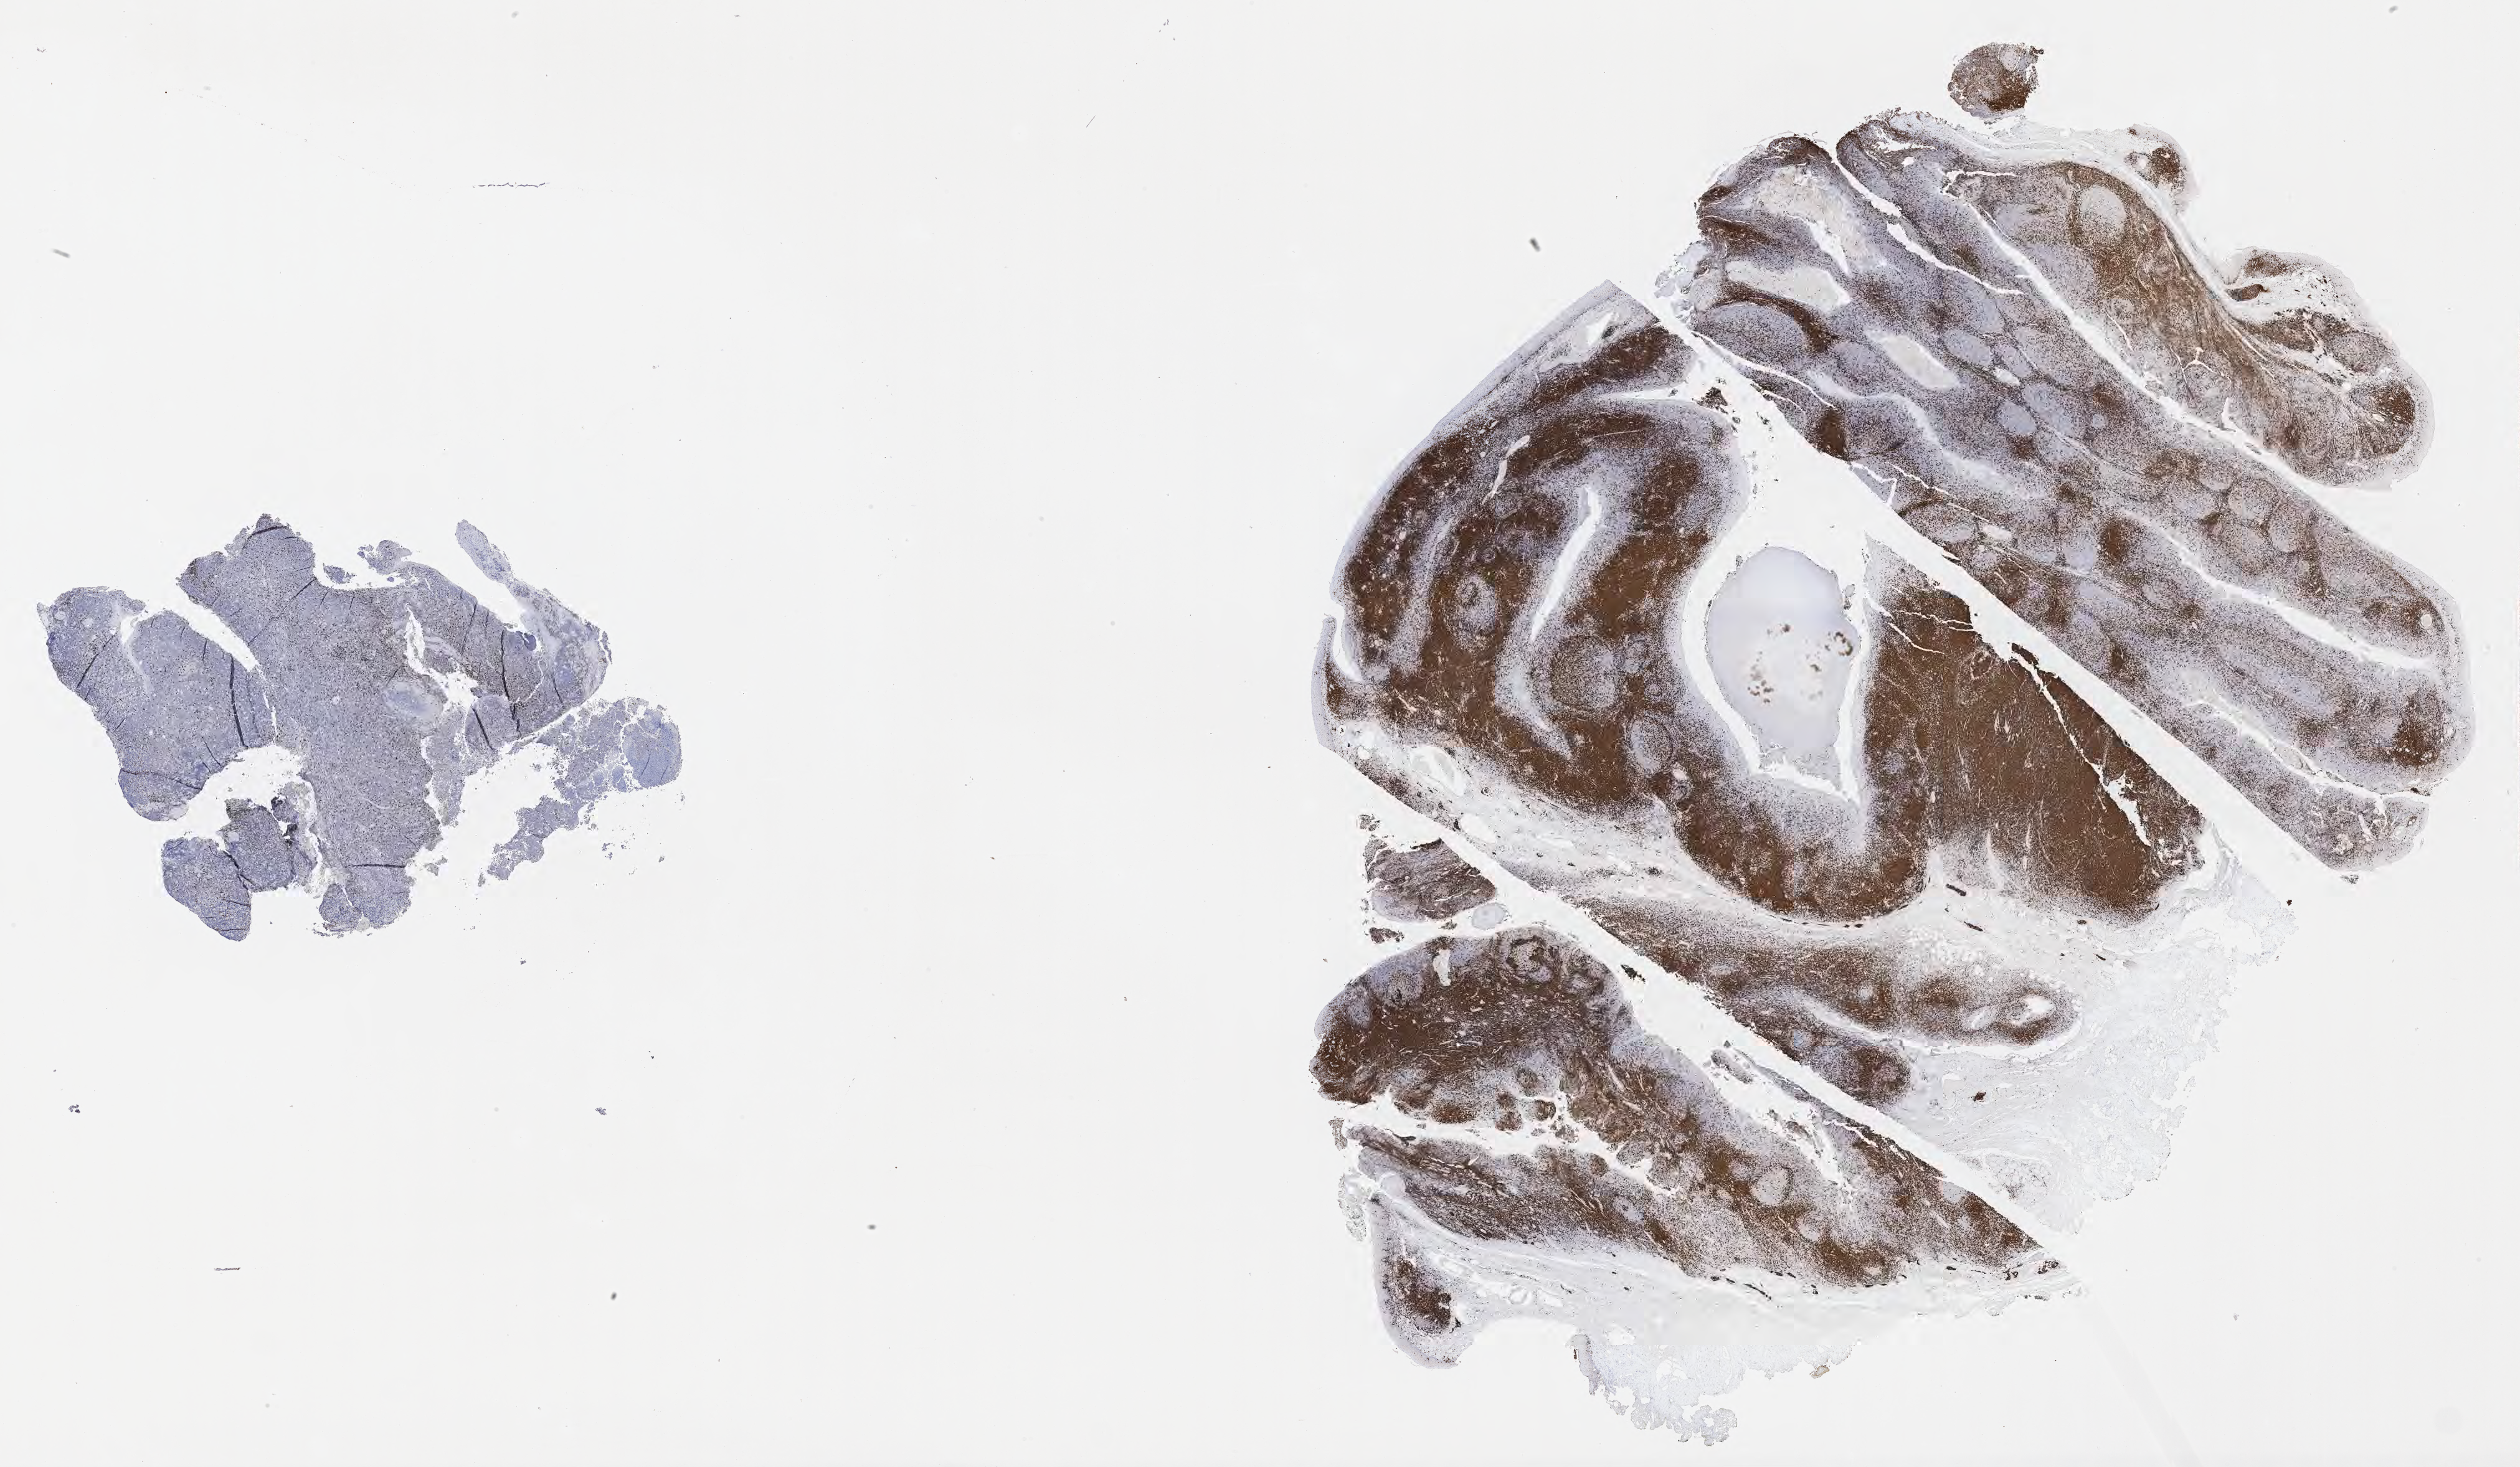
Whole-slide image, immunohistochemical stain for CD3 — low-resolution overview of the scanned area, about 32.7 x 19.0 mm, tumor tissue. Male patient; age at initial diagnosis 3 years.
Histologic diagnosis: Burkitt lymphoma, NOS.